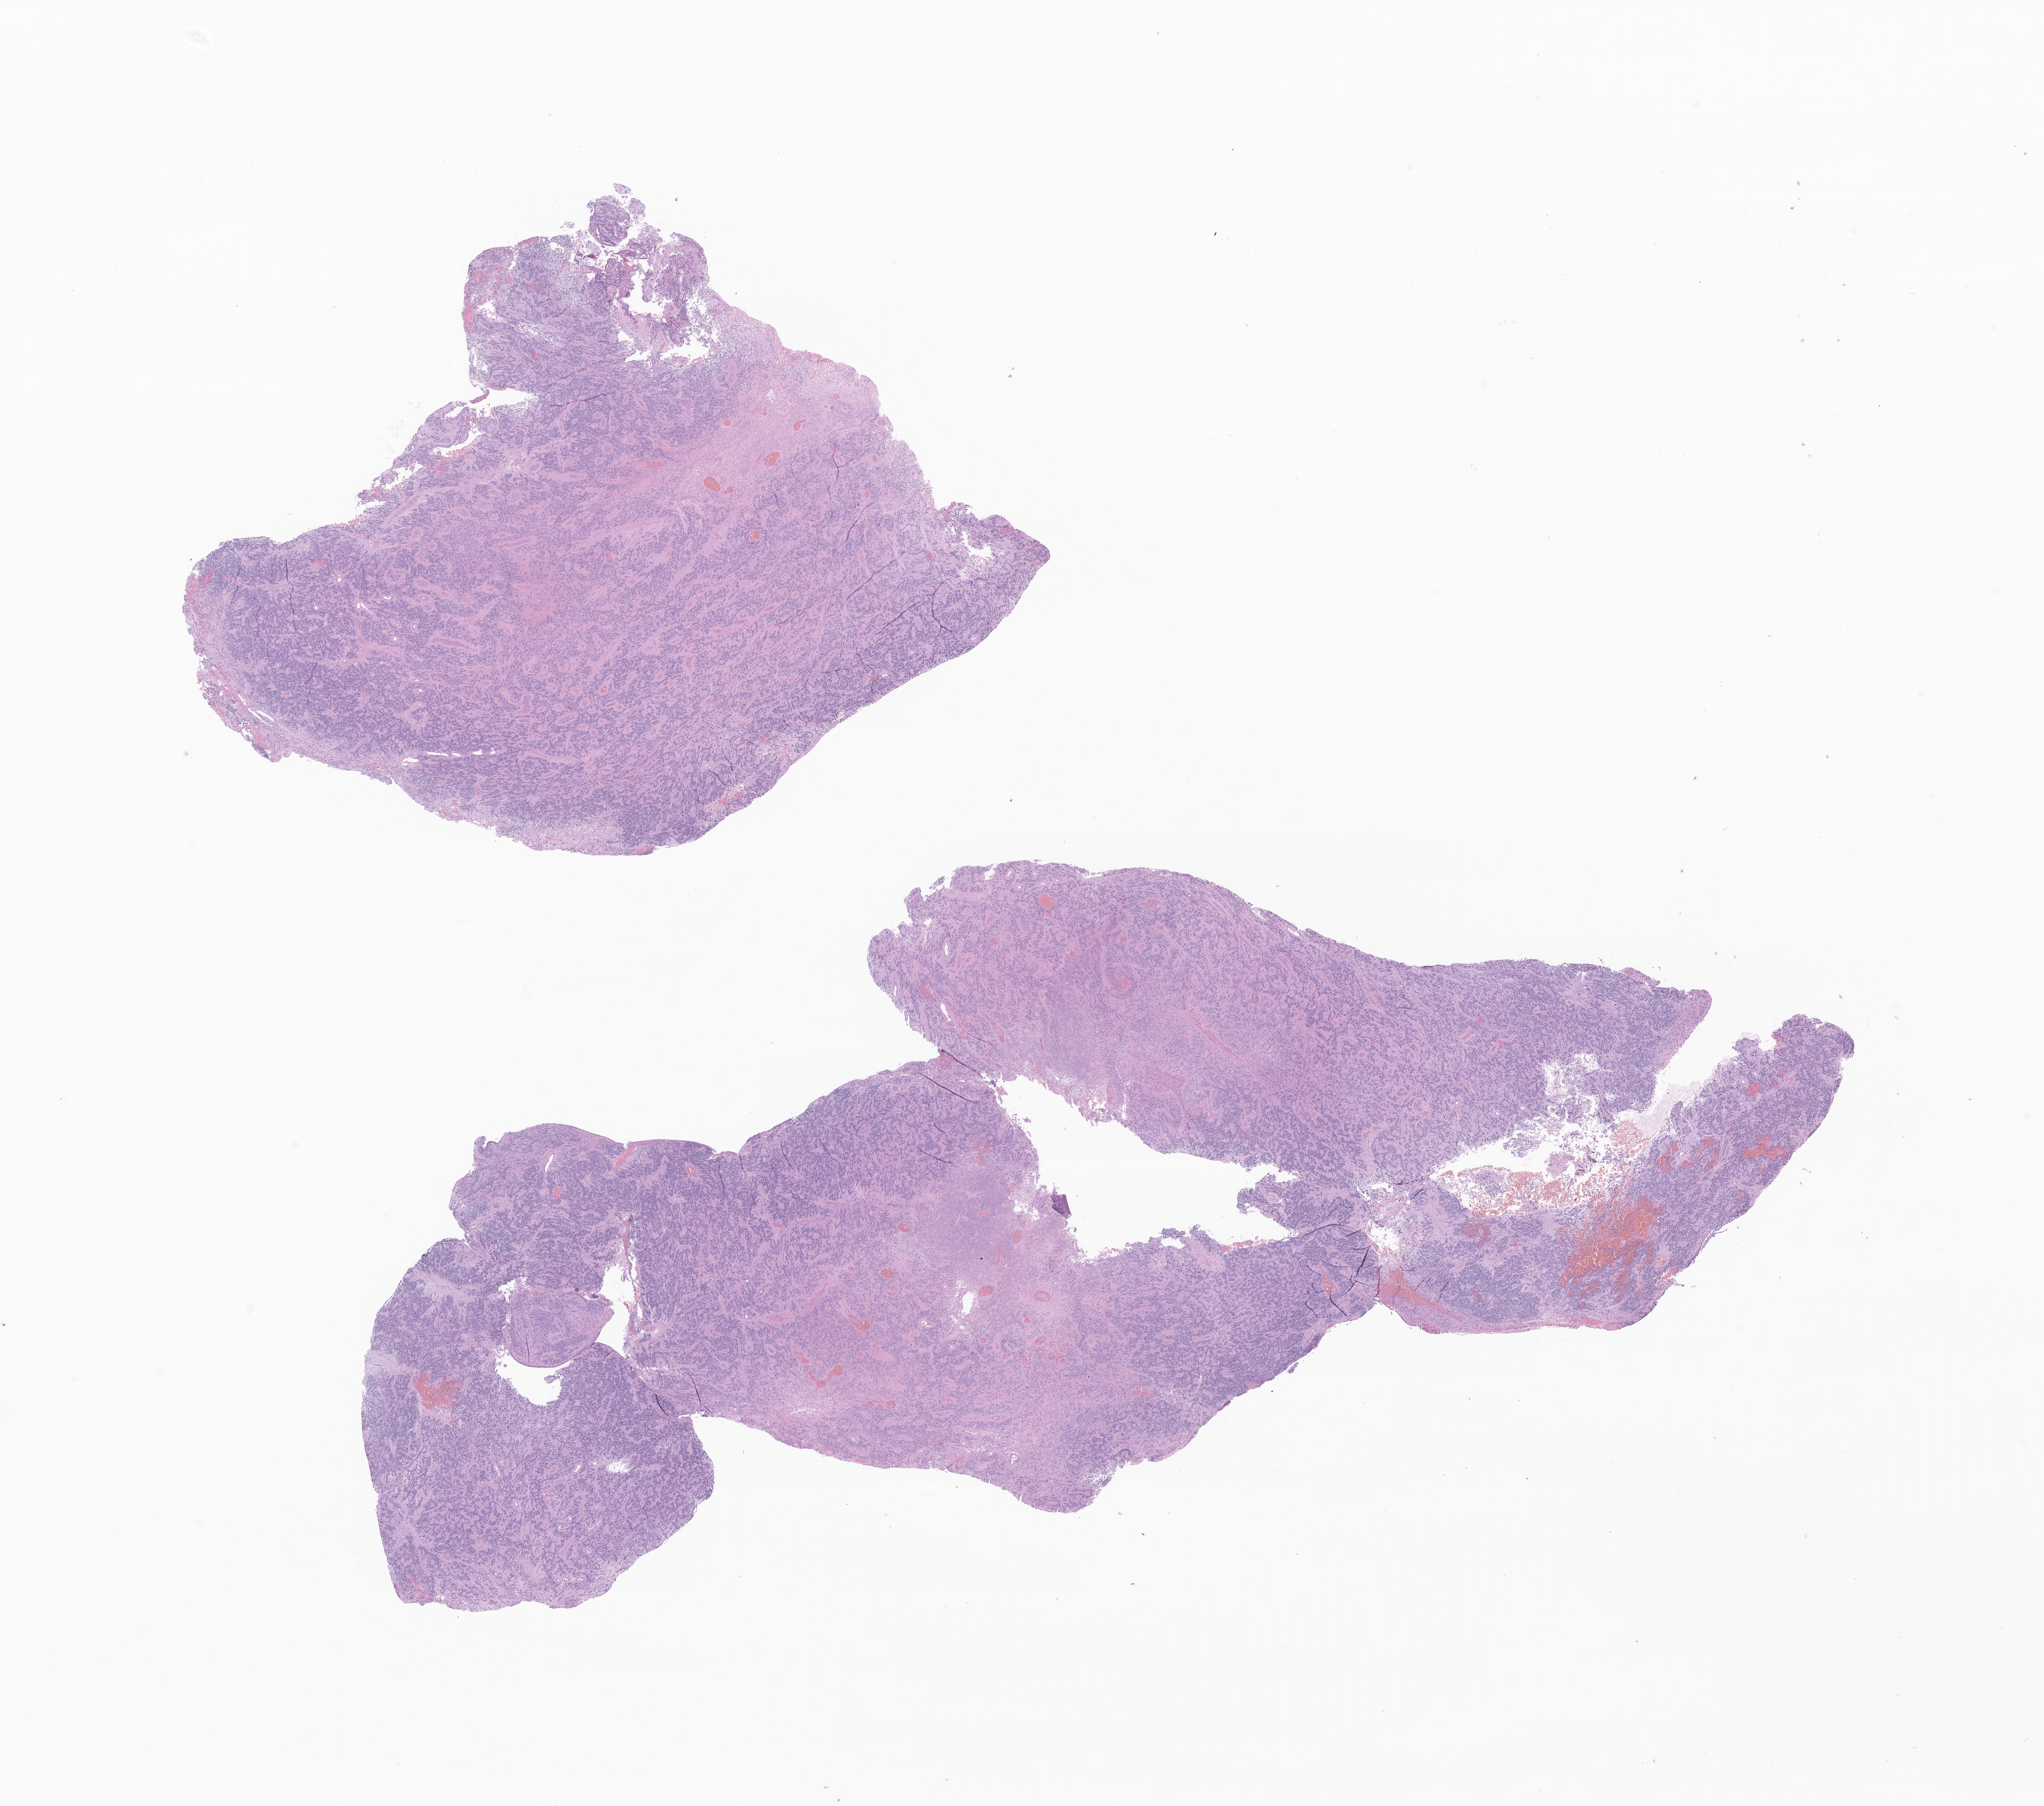
Hematoxylin and eosin (H&E) whole-slide image of tumor tissue from the brain, whole scanned area (about 20.2 x 17.9 mm) shown as a low-resolution overview, formalin-fixed, paraffin-embedded (FFPE) tissue. Patient: female, age 835 days (about 2.3 years).
* diagnosis: Neoplasm, uncertain whether benign or malignant